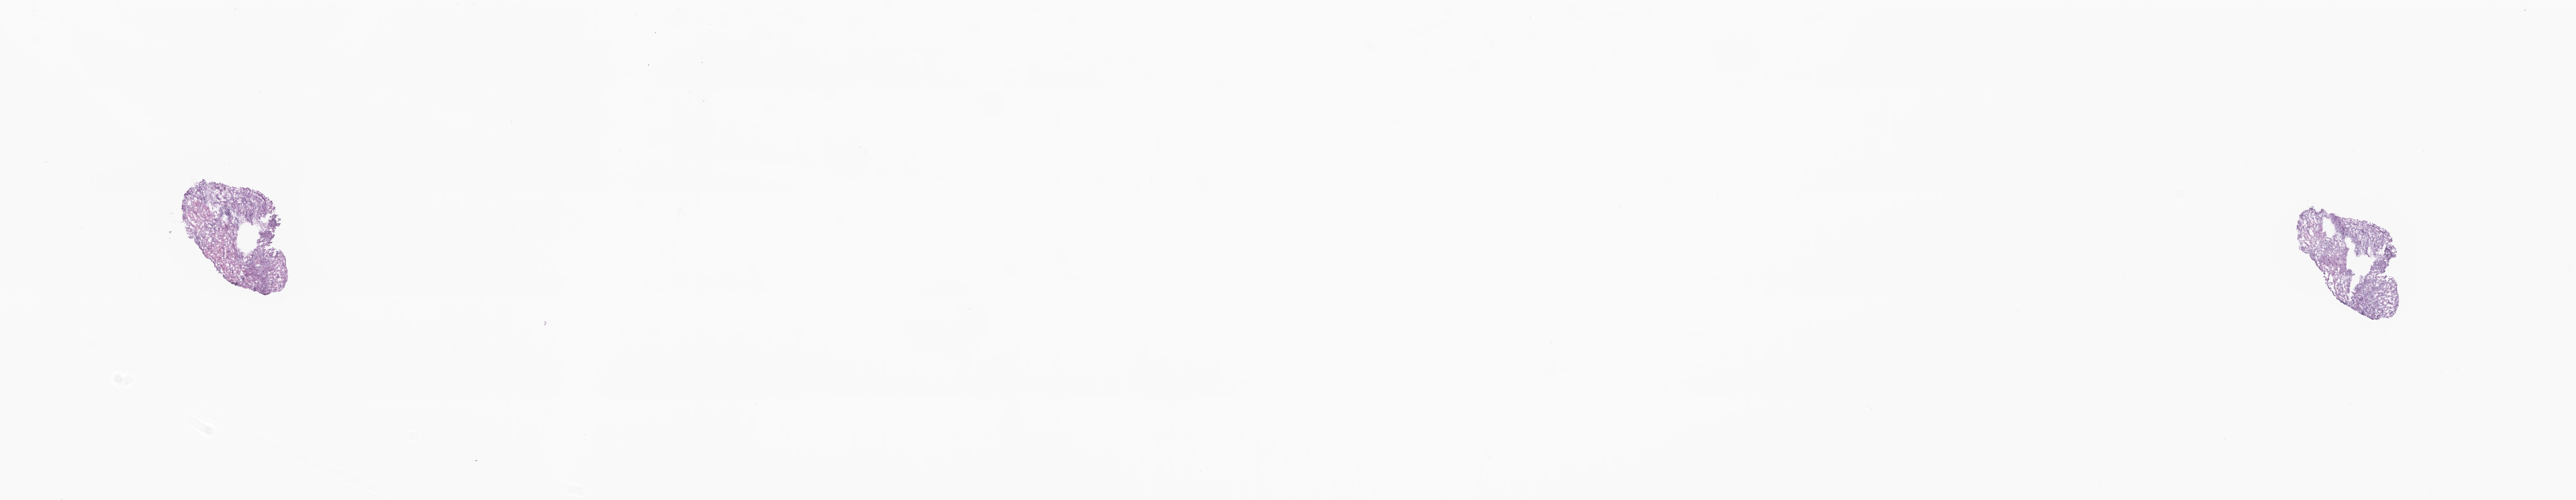
Digitized hematoxylin and eosin (H&E)-stained section, shown as a low-resolution overview of the whole scanned area (about 26.7 x 5.2 mm). Cryosection. Specimen: primary tumor. Site: endometrium. Patient sex: female. Pathologist review of this section (percent, as recorded): tumor cells 85%, tumor nuclei 85%, stromal cells 15%, necrosis 0%, normal cells 0%. Infiltration values recorded for this section: lymphocyte infiltration 2%, monocyte infiltration 2%, neutrophil infiltration 4%.
* diagnosis: Serous carcinoma, NOS
* AJCC pathologic stage: Stage IIIC2
* section: top of the tissue portion